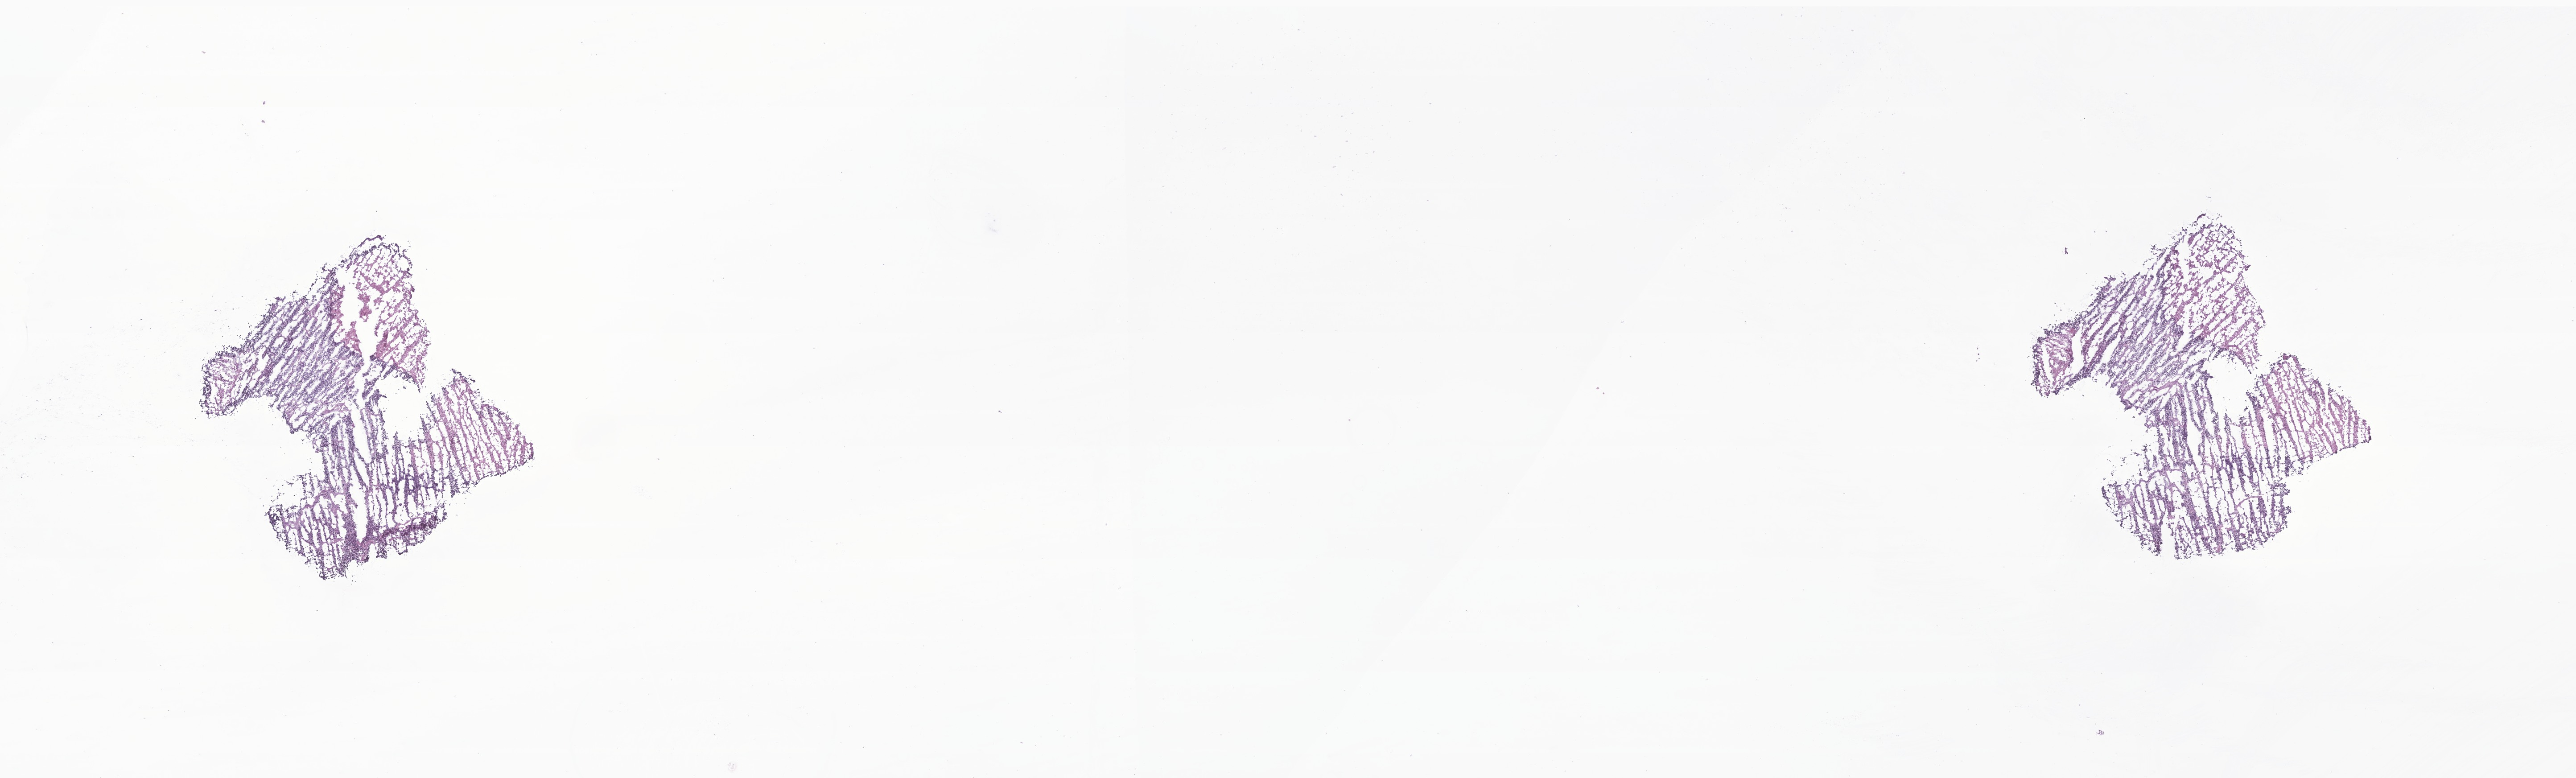
H&E whole-slide image of tumor tissue from the retroperitoneum, whole scanned area (about 24.4 x 7.4 mm) shown as a low-resolution overview. Cryosection (OCT / tissue freezing medium). Female patient, age 37 months (3 years 1 month).
* recorded diagnosis: Neuroblastoma, NOS